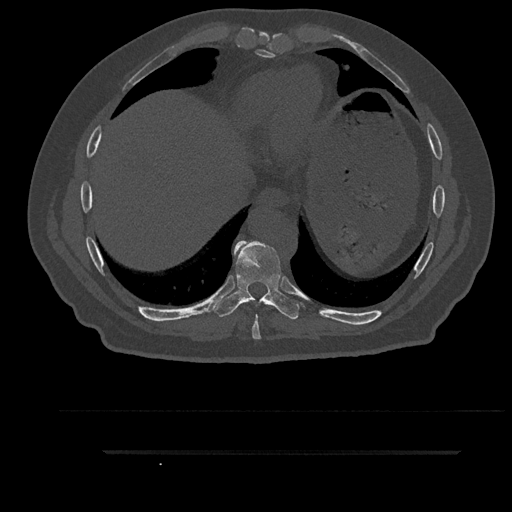
CT including the spine, one axial slice; 120 kVp; bone window (W 1800 / L 400 HU); 0.5 mm slice thickness; 512 × 512 image matrix, field of view 432 × 432 mm. Patient: male, 63 years. Case-level facts recorded for this patient, not image findings: primary cancer: renal; vertebrae with lytic lesions (as recorded): T8.
Annotated regions visible in this slice (semi-automatic segmentation, software-assisted and operator-edited):
- T8 vertebra: box from (x=252, y=315) to (x=261, y=340) px
- T9 vertebra: (x=212, y=241)–(x=300, y=319)